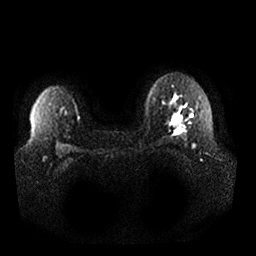
Breast MRI, one axial slice; diffusion-weighted series; image 2 of 4 stored at this slice position (different b-values; order by instance number); 1.5 T; 4 mm slice thickness; 256 × 256 image matrix. Female patient.
Outlined on this slice (outlined manually by an expert reader):
- tumour on diffusion-weighted imaging: bounding box (x1, y1, x2, y2) in pixels: (170, 115, 182, 129)